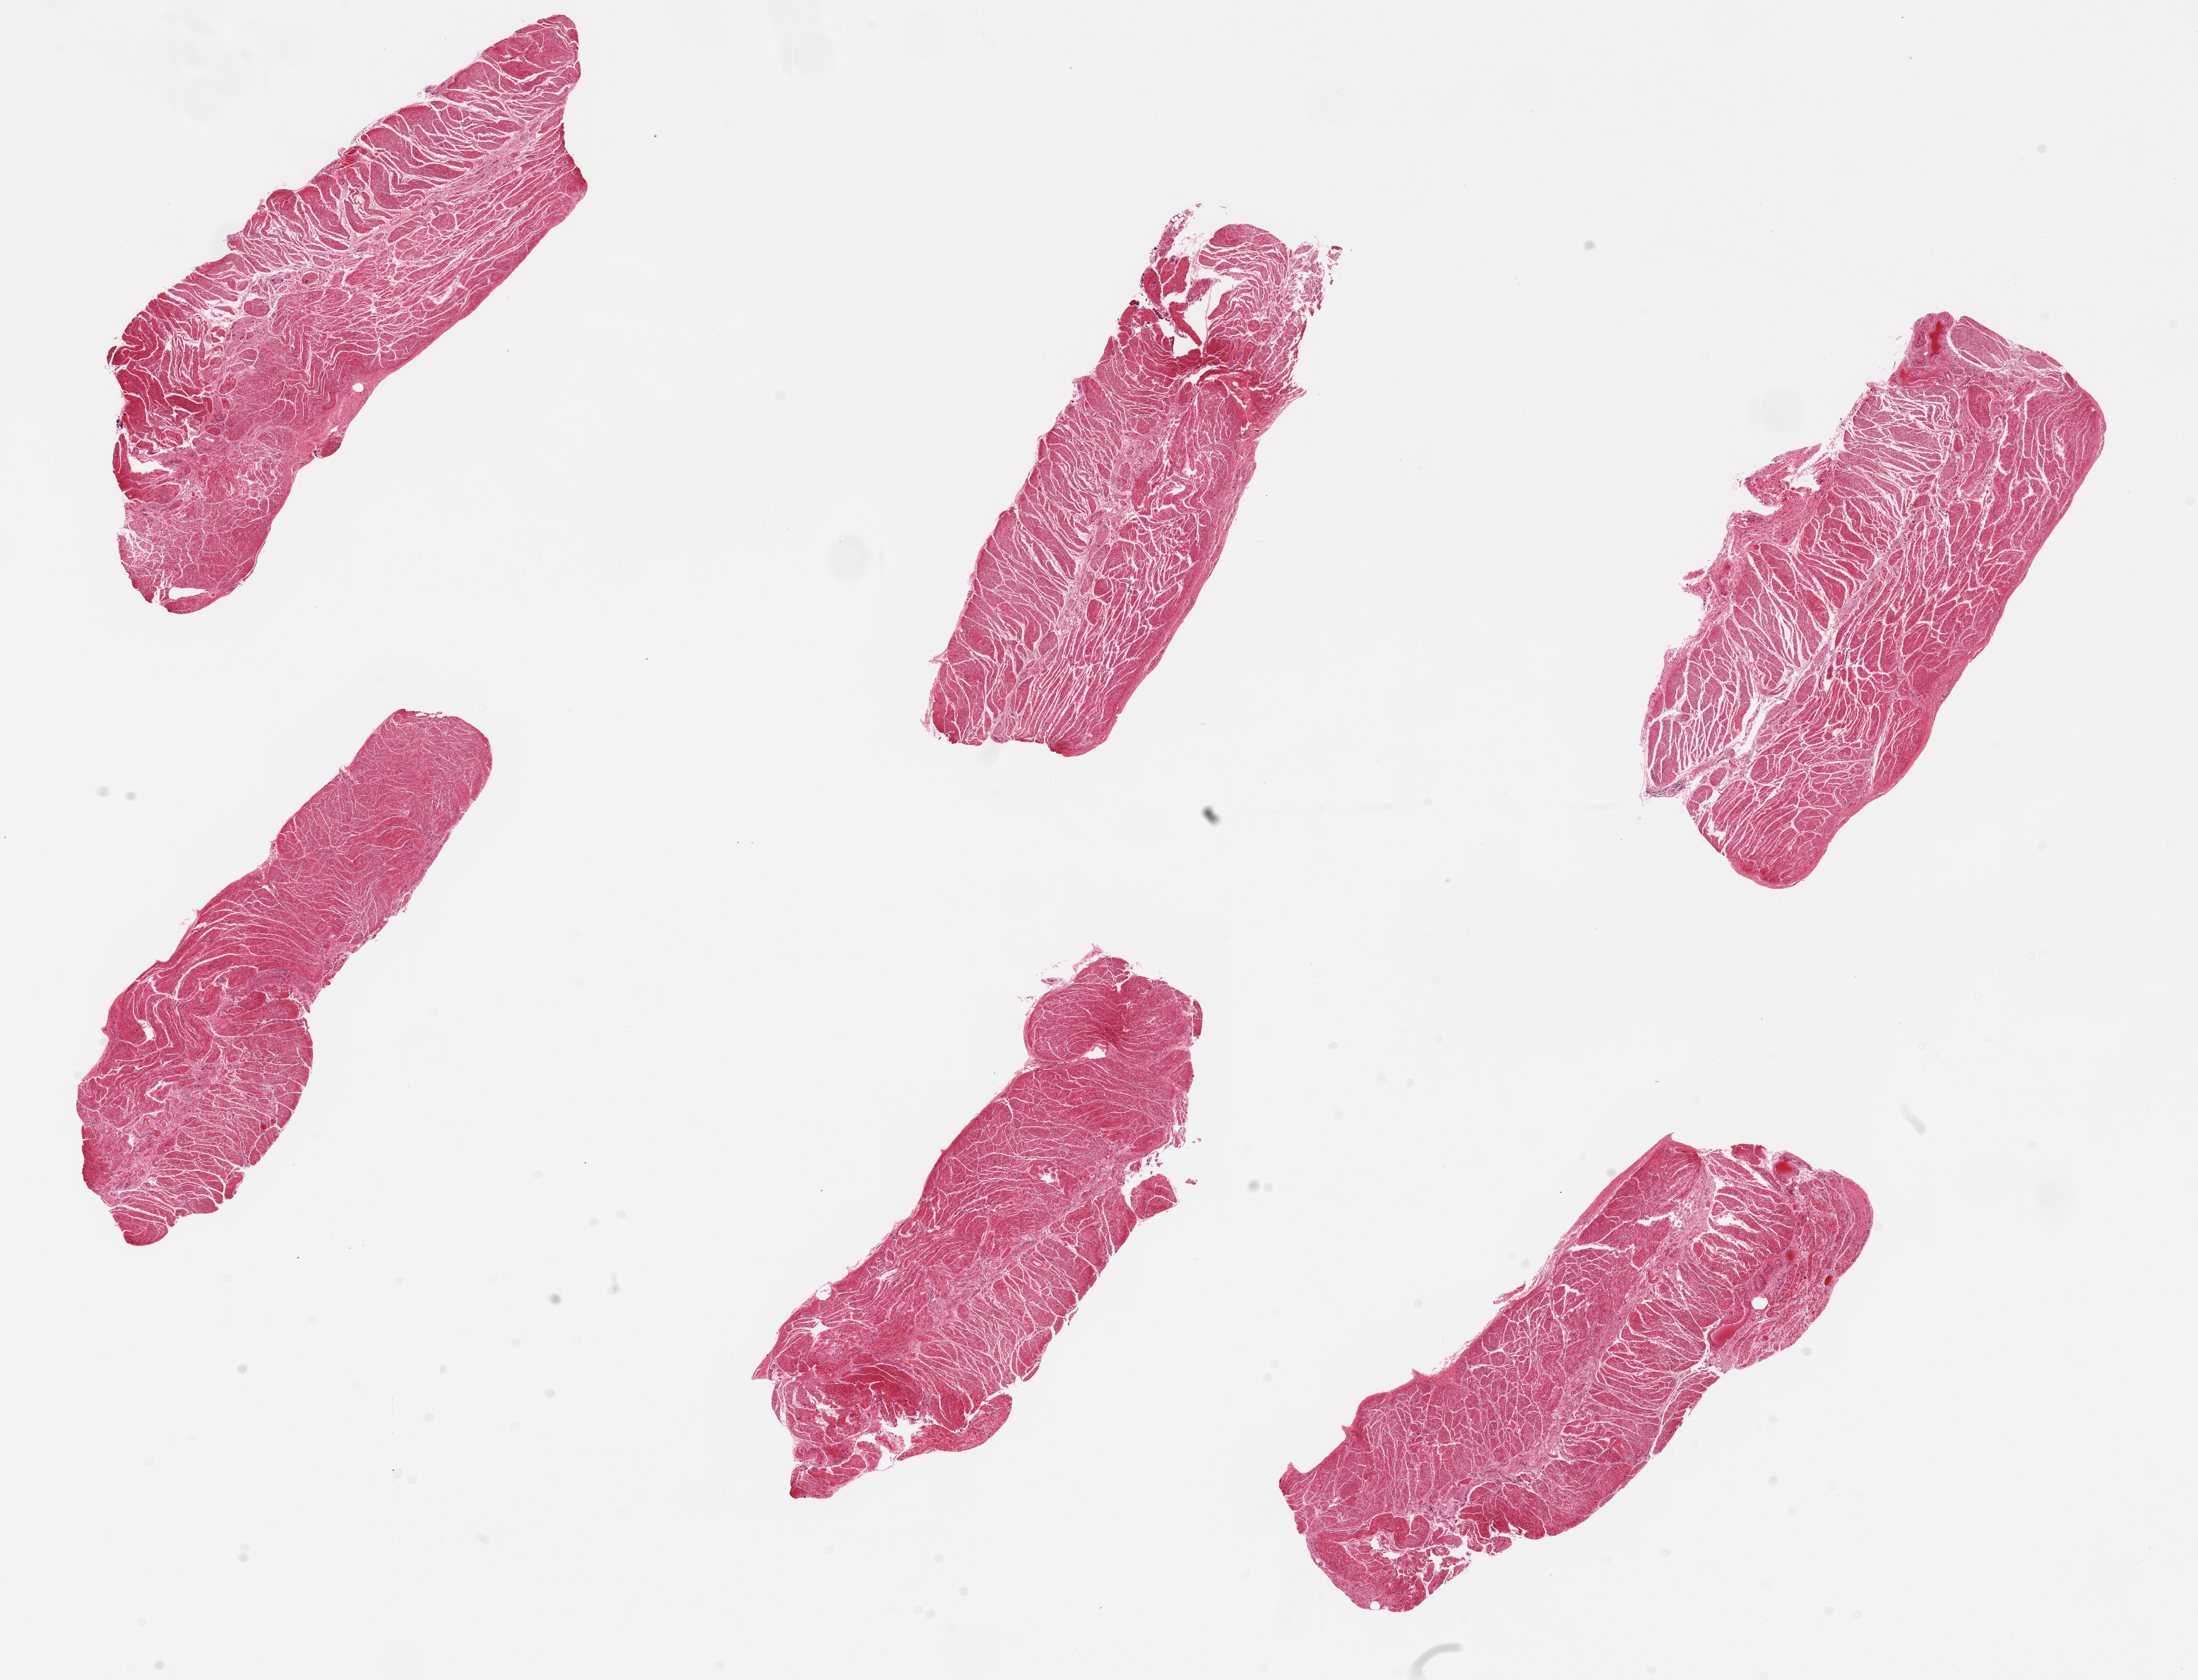
Haematoxylin and eosin whole-slide image, brightfield — shown as a low-resolution overview of the whole scanned area (about 24.6 x 18.8 mm). PAXgene-fixed paraffin-embedded (PFPE) section. Section of esophageal muscle (target tissue). Tissue donor sample. Donor: female.
Pathologist's review note for this sample: 6 pieces; well trimmed-all muscle.